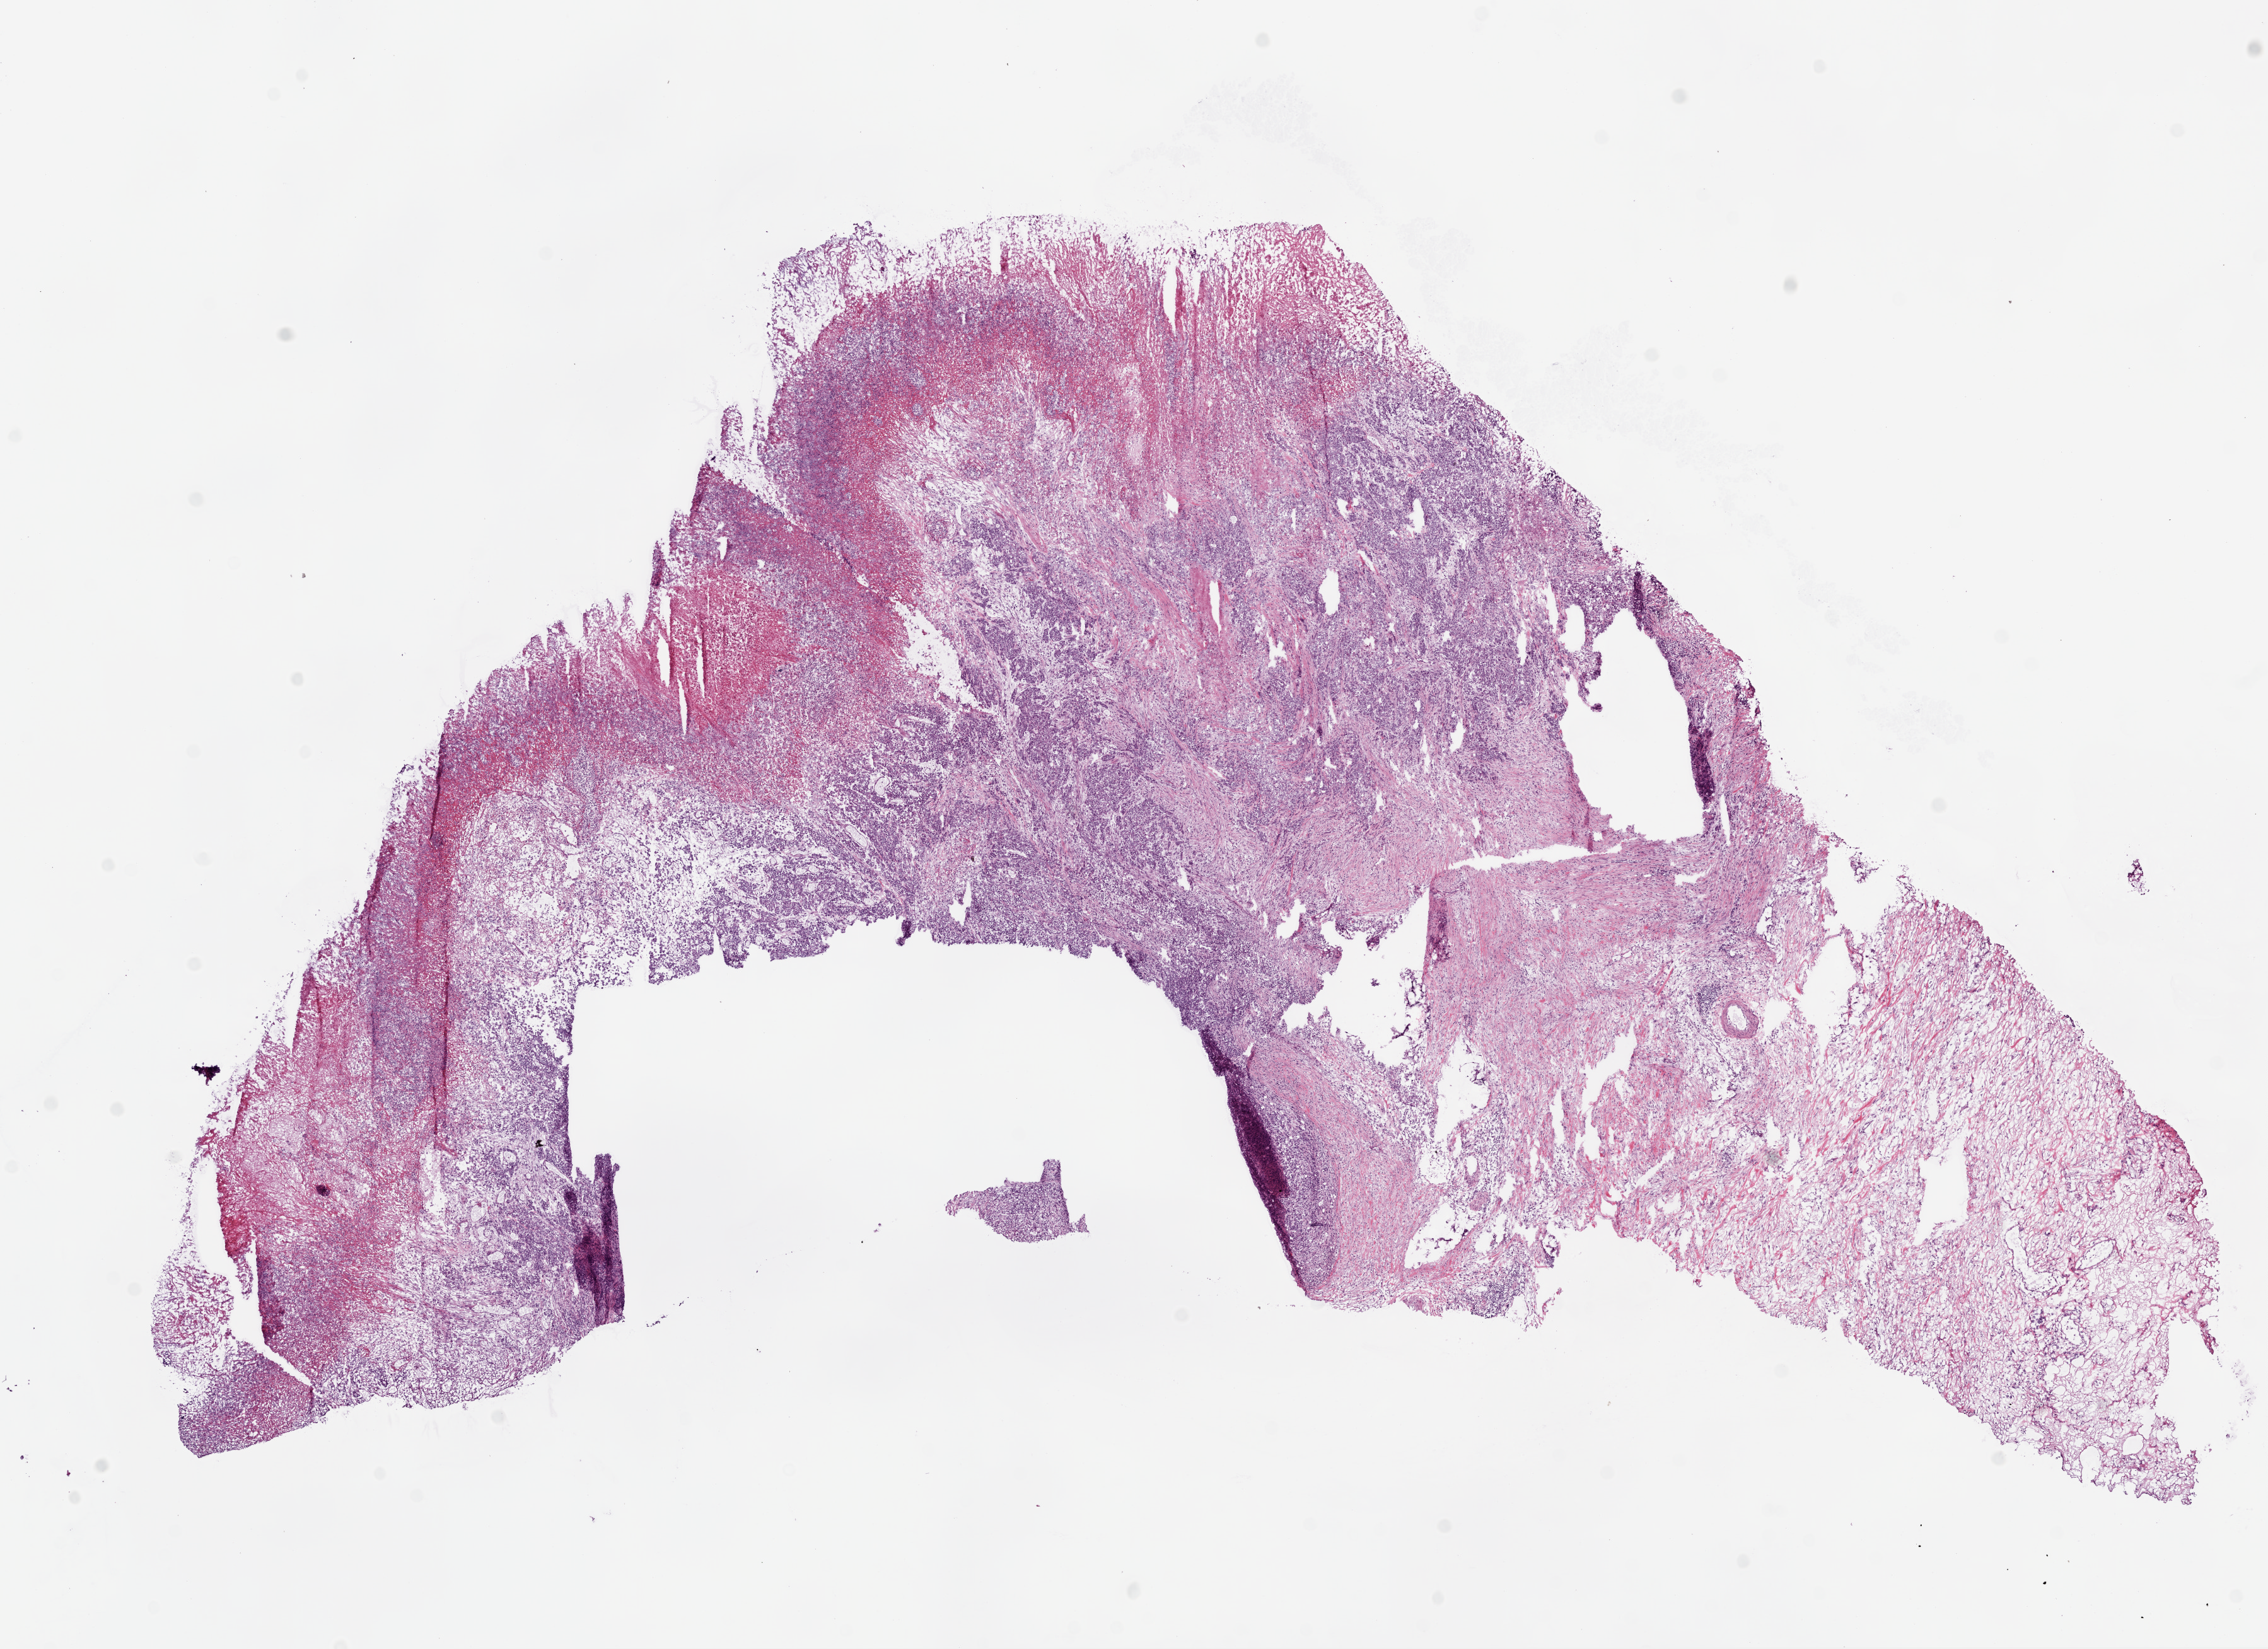
Digitized H&E-stained tissue section (whole slide), shown as a low-resolution overview of the whole scanned area (about 14.5 x 10.5 mm); frozen section; stomach, primary tumour sample. Female, age 51 years at initial diagnosis.
Diagnosis: Carcinoma, diffuse type.